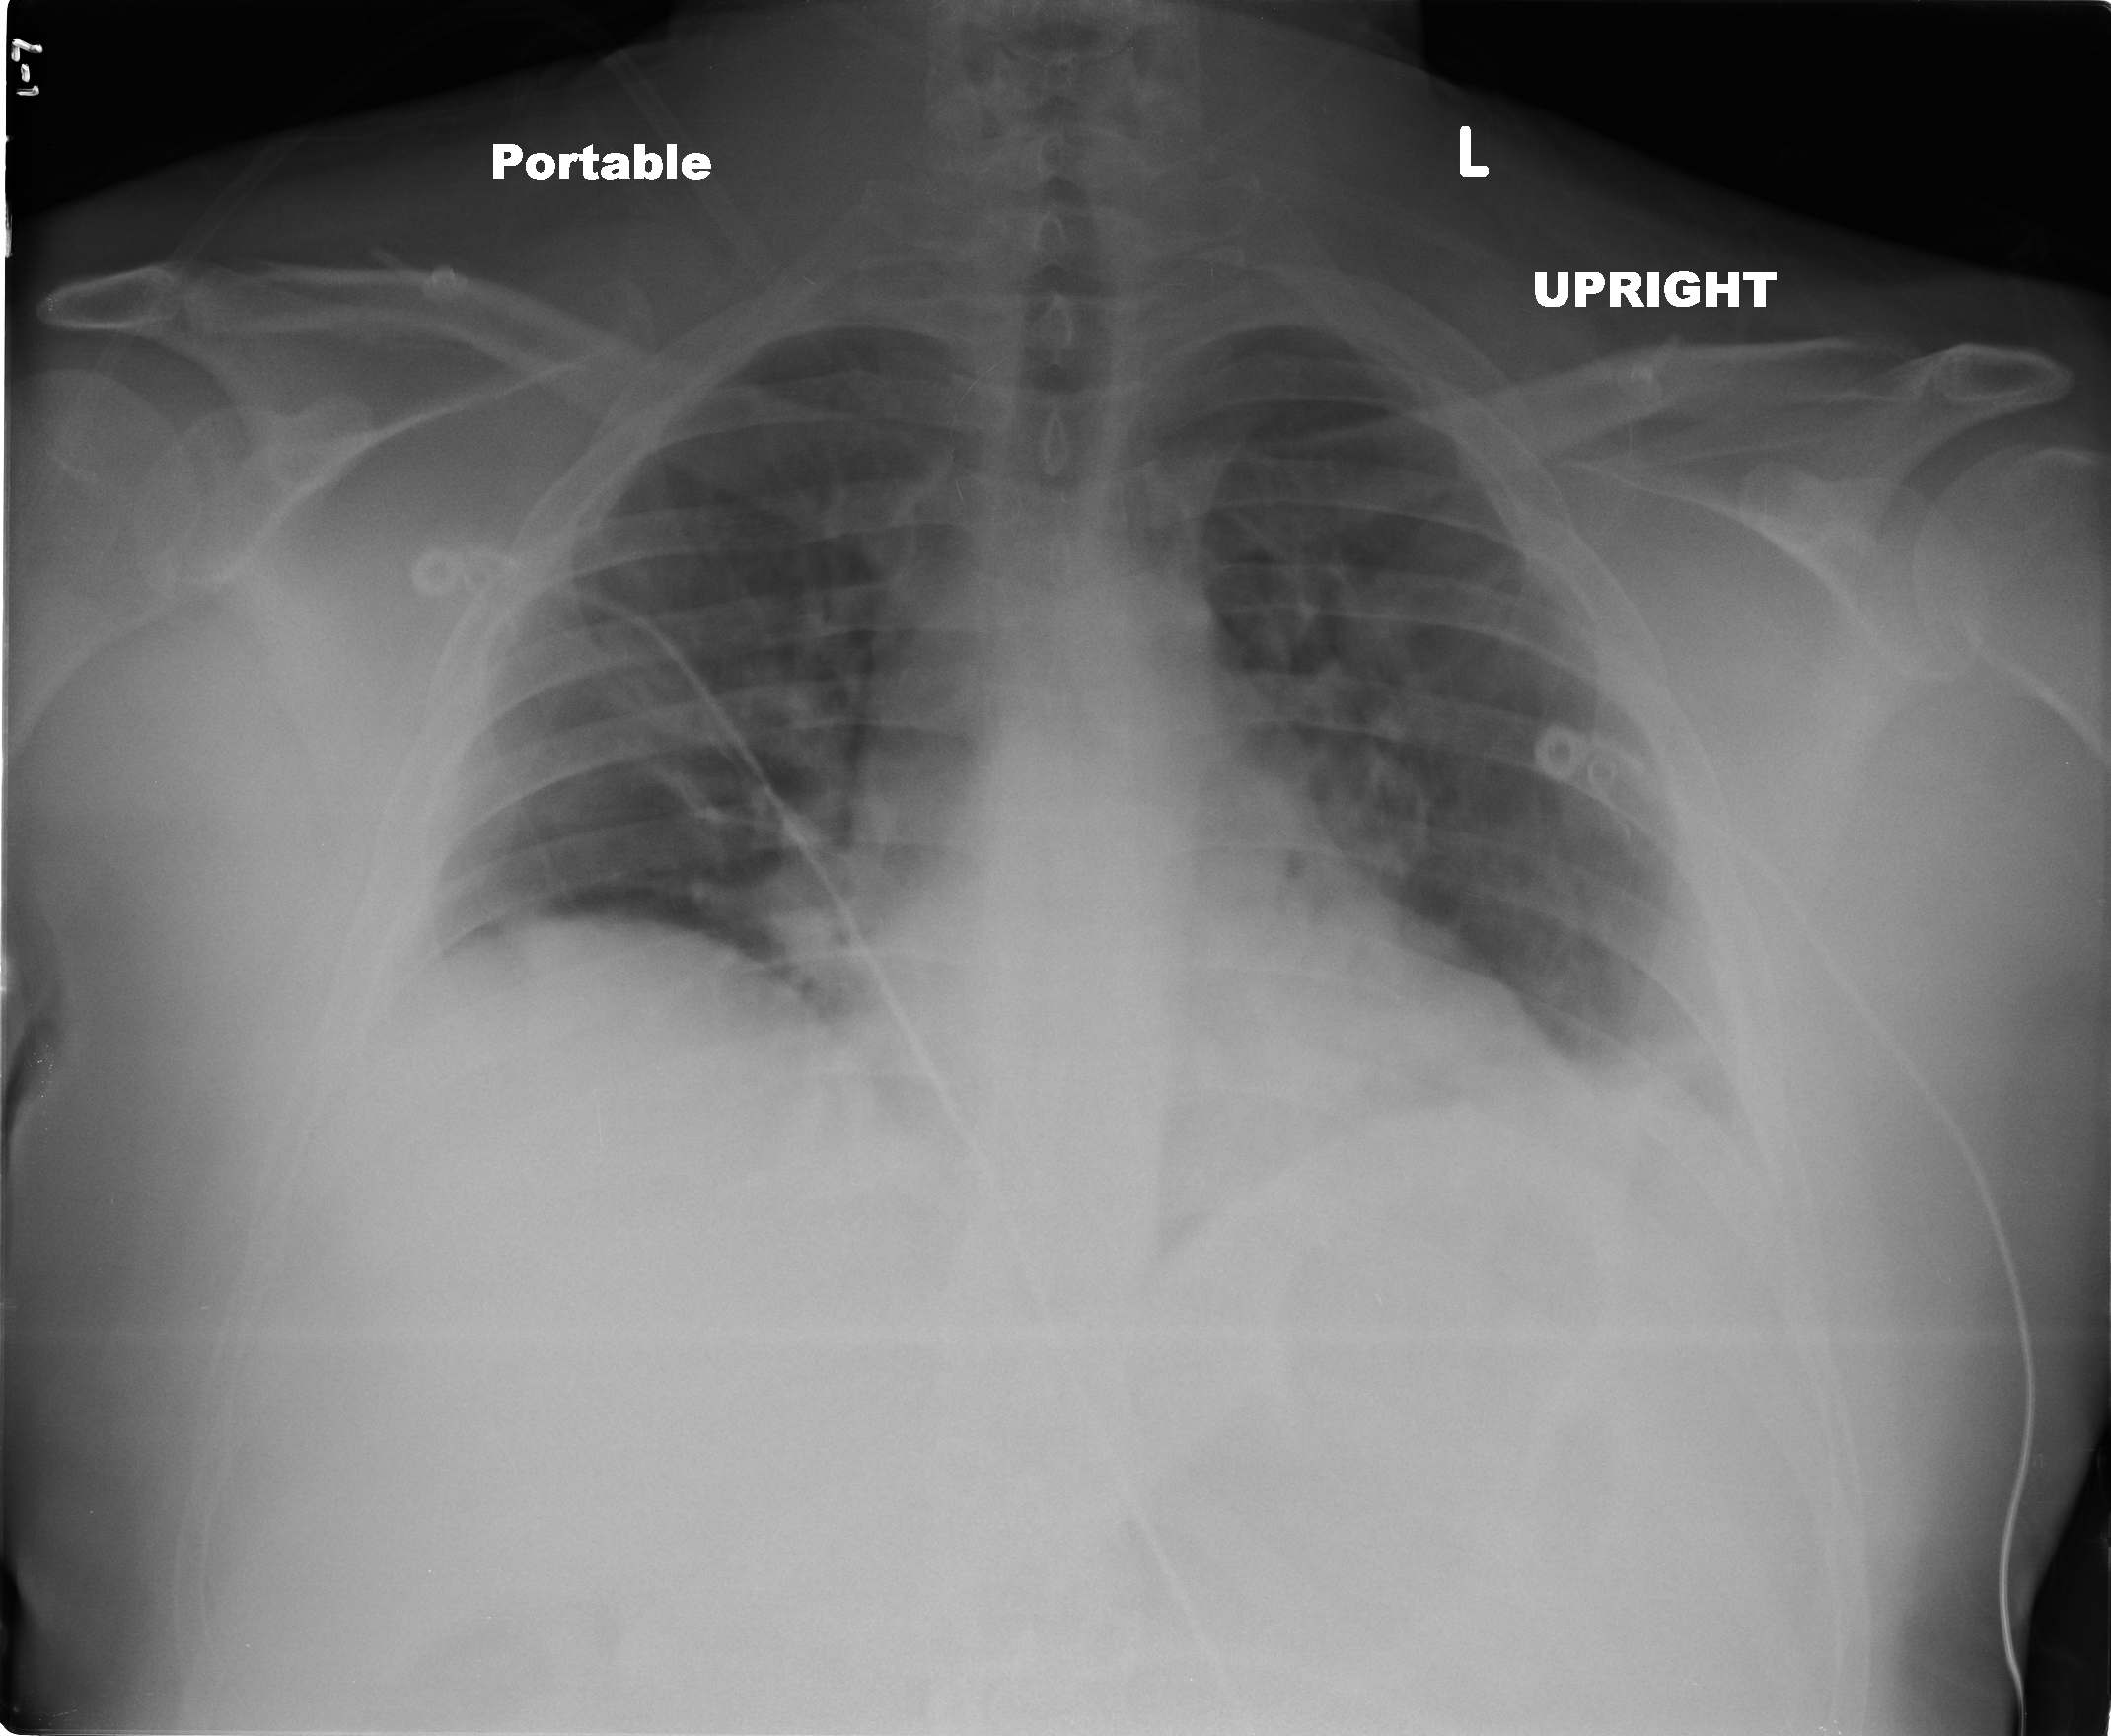
Portable chest radiograph, AP projection. Male patient, age 39 years; imaged 0 days after the COVID-19 diagnosis.
Radiologist key findings (as recorded): Bibasilar opacities are seen most pronounced on the left. No large pleural effusion identified.